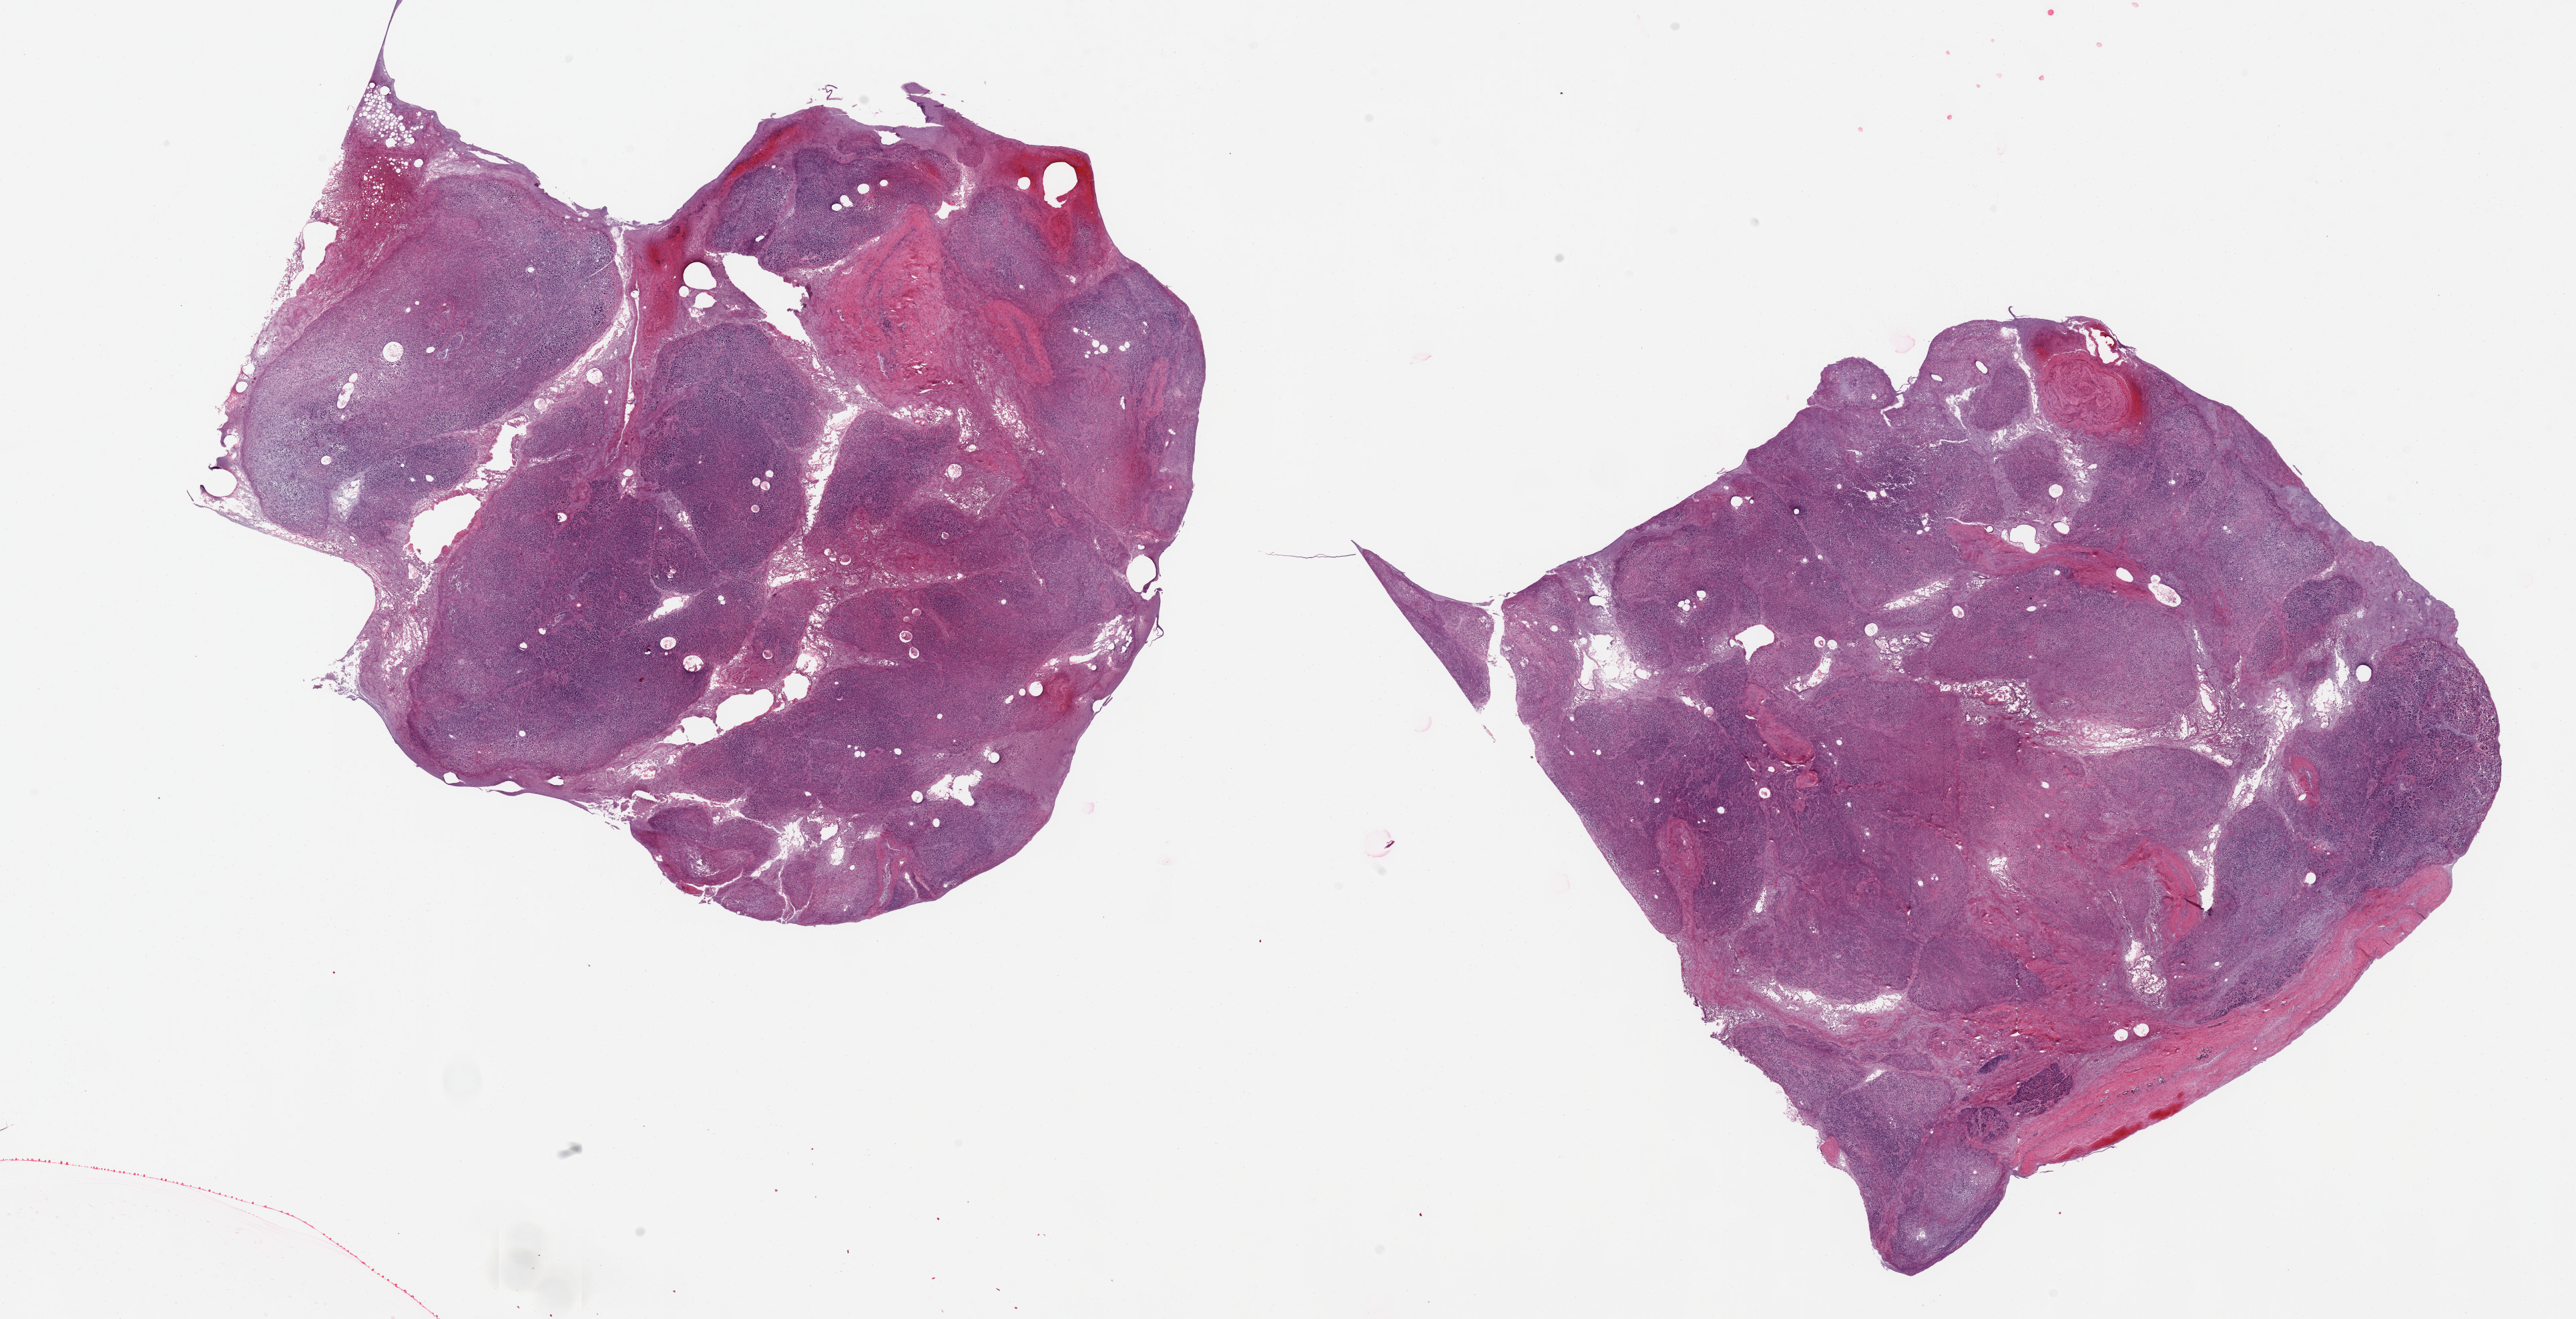
Digitized haematoxylin and eosin-stained section, shown as a low-resolution overview of the whole scanned area (about 30.5 x 15.6 mm, from a 20x scan). PAXgene-fixed, paraffin-embedded tissue. Target tissue: pancreas. Tissue donor sample. Donor: female.
- reviewer comment on this tissue sample: 2 ~10x9mm aliquots, marked diffuse saponification/autolysis